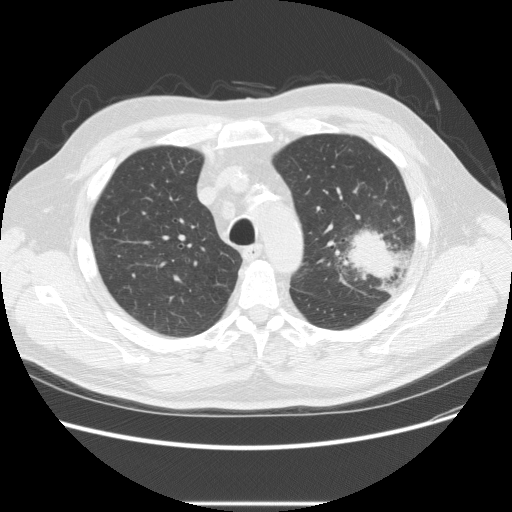
Low-dose screening chest CT, one axial slice. Slice 172 of 233 in the series (ordered by position). 120 kVp. Lung window (W 1500 / L -600 HU). 2.5 mm slice thickness. 512 × 512 image matrix, field of view 380 × 380 mm.
Outlined on this slice (manually delineated by an expert):
- lesion 1 (tumor, upper lobe of left lung): box from (x=343, y=226) to (x=400, y=283) px